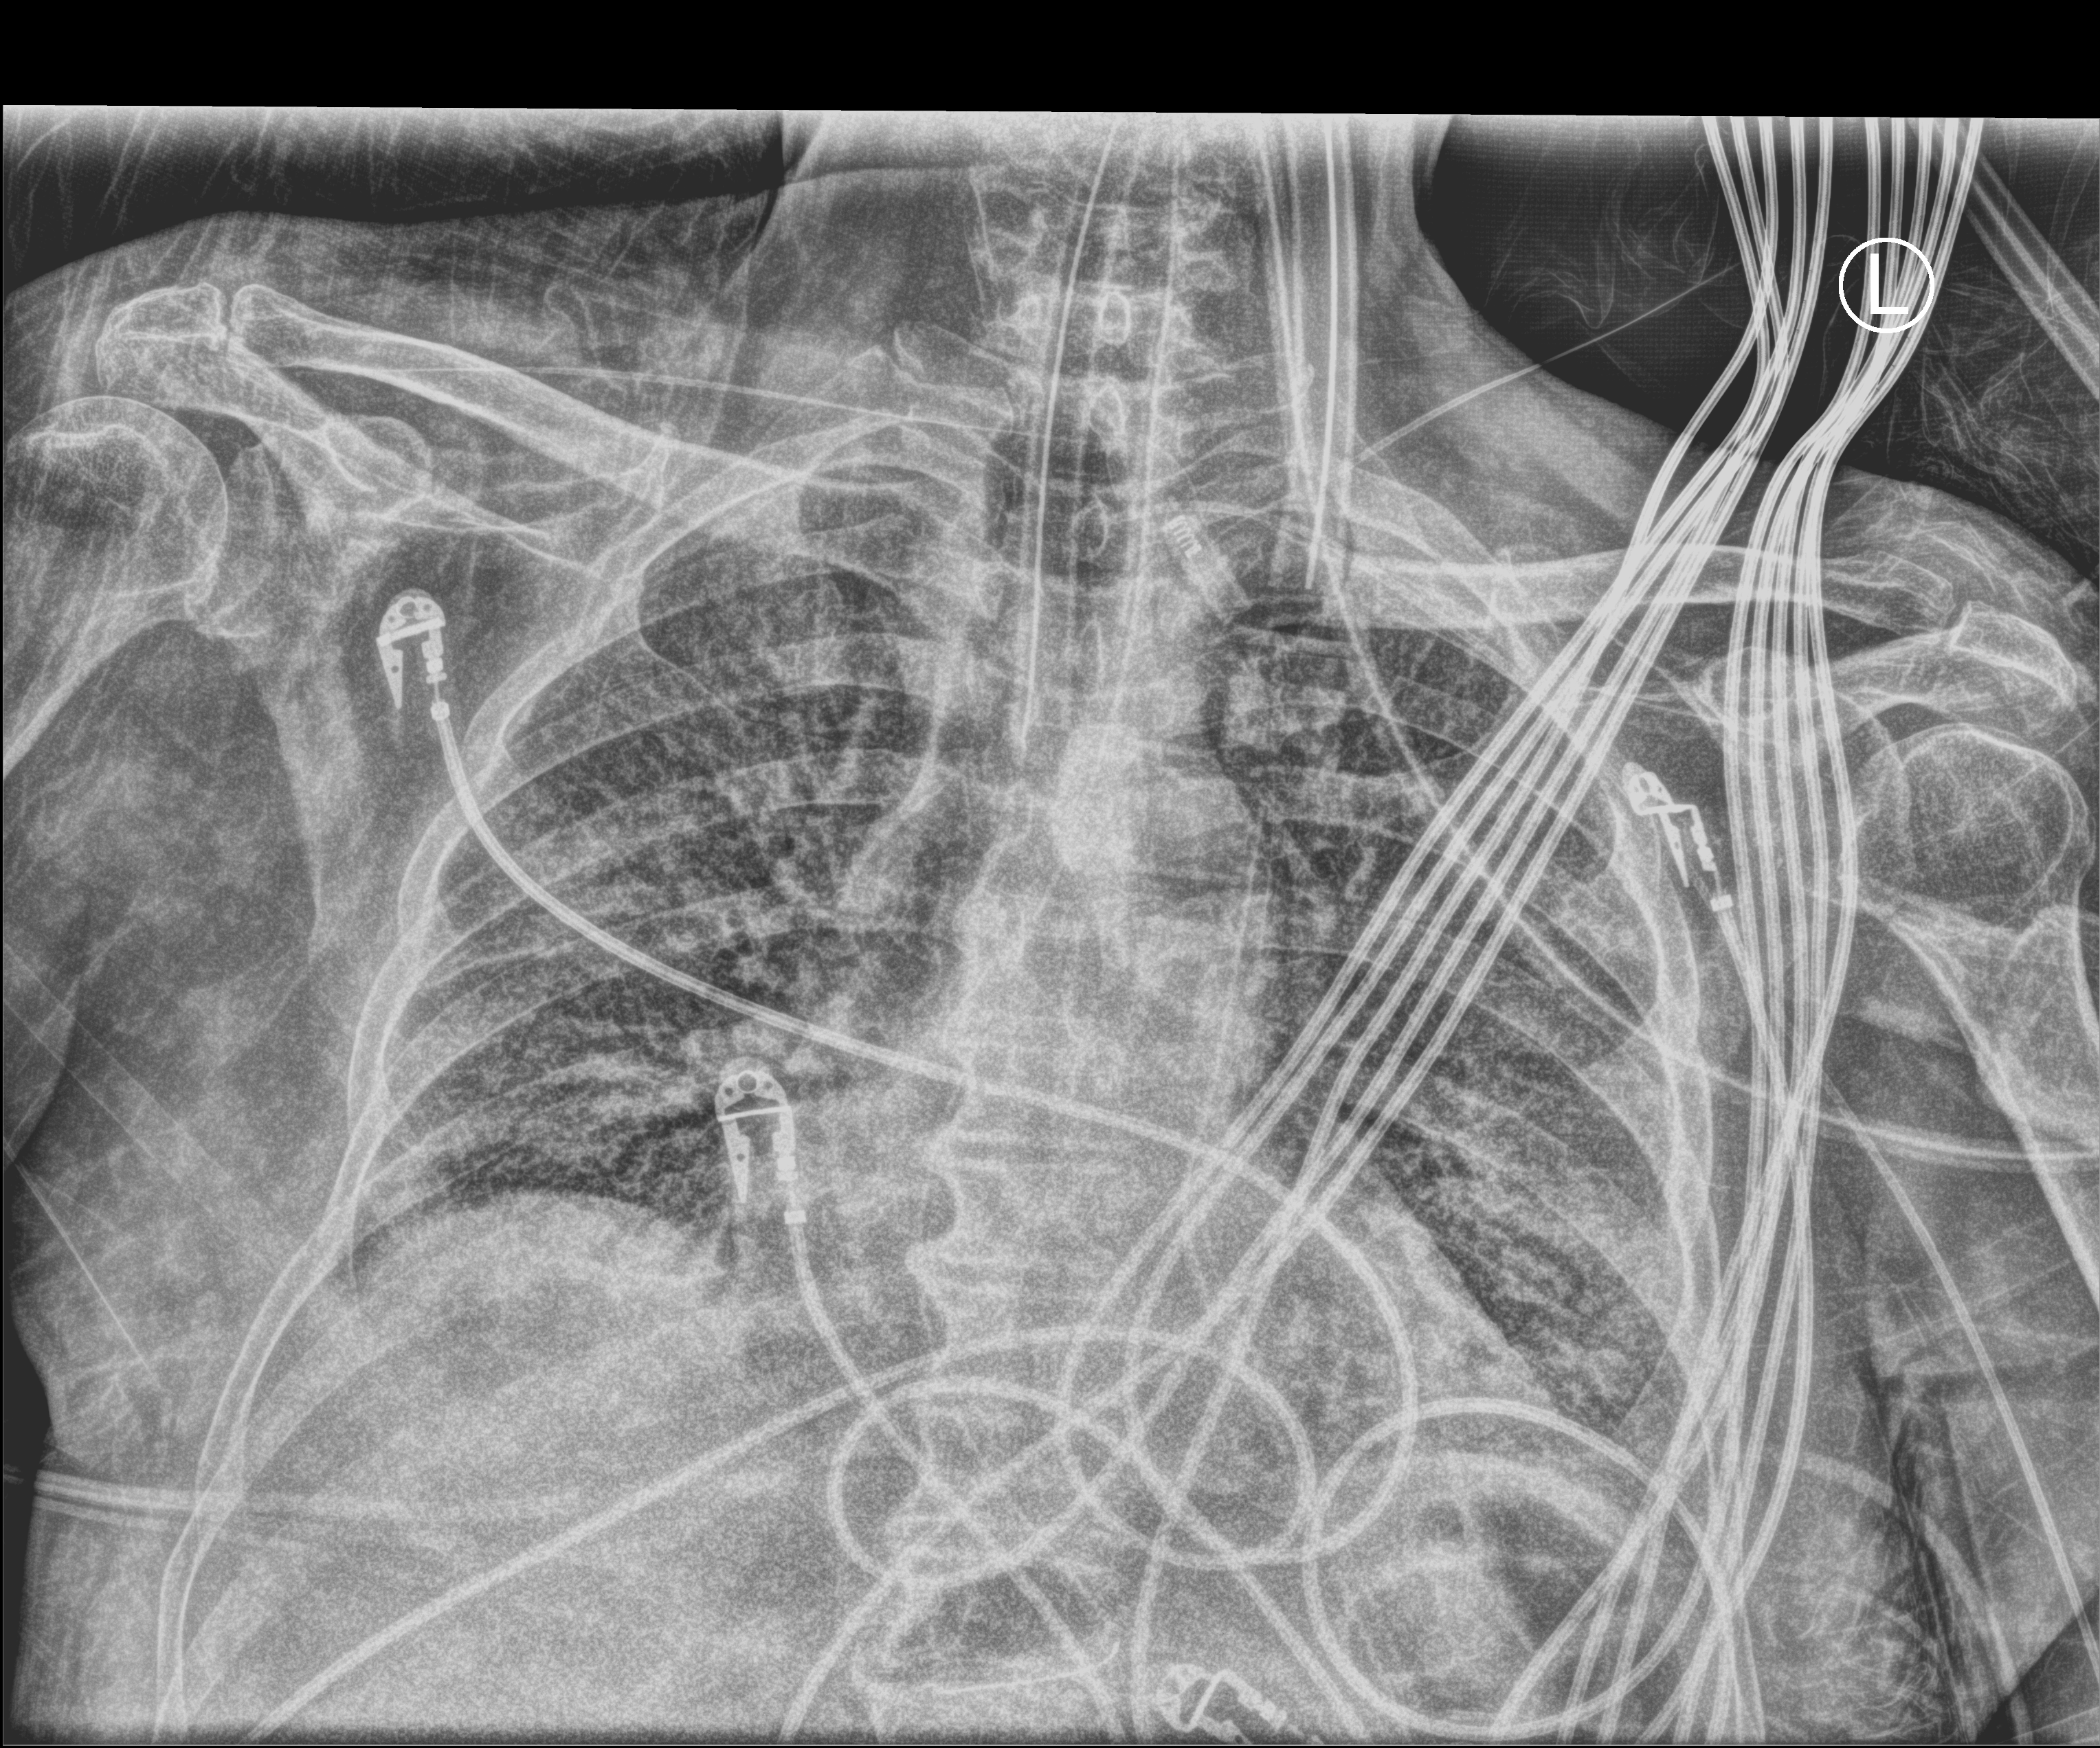
Portable chest radiograph, anteroposterior (AP) projection. Male patient hospitalised with COVID-19, age 75–90 years.
From the hospital-stay record, not from the radiograph (when in the stay this image was taken is not recorded):
- length of hospital stay: 30 days